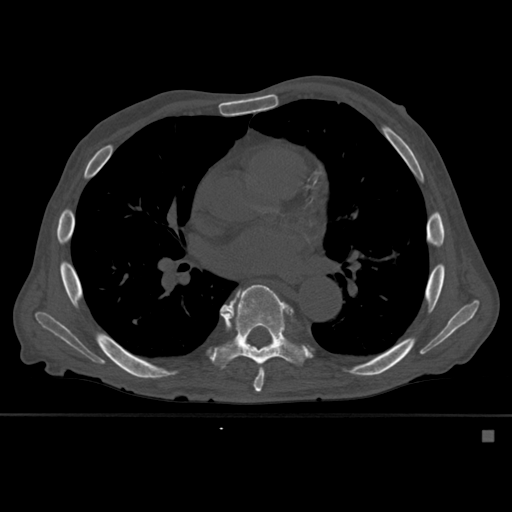
CT including the spine, one axial slice. Position 353 of 527 along the scan axis. Bone window (W 1800 / L 400 HU). 1.5 mm slice thickness. 512 × 512 image matrix. Patient: male, 78 years. Case-level facts recorded for this patient, not image findings: primary cancer: prostate.
Structures marked on this image (semi-automatic segmentation, software-assisted and operator-edited):
- T7 vertebra: bounding box (x1, y1, x2, y2) in pixels: (226, 290, 264, 392)
- T8 vertebra: (211, 284, 307, 369)